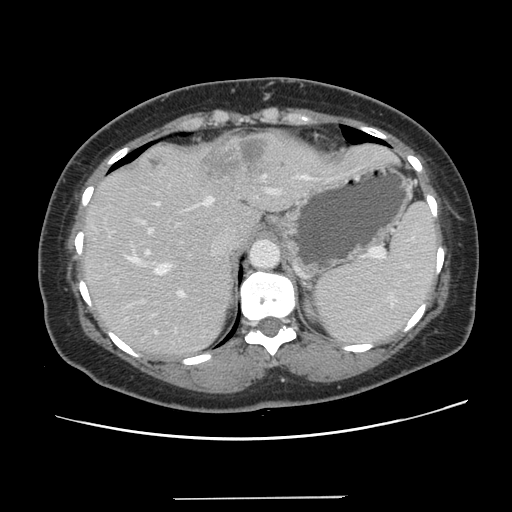
Contrast-enhanced abdominal CT, one axial slice; position 98 of 141 along the scan axis; intravenous contrast given; soft-tissue window (W 400 / L 40 HU); 512 × 512 image matrix, field of view 366 × 366 mm. Female patient, age 53 years. From the clinical record (not read from this slice): diagnosis: colorectal cancer liver metastases, imaged before liver resection; multiple liver metastases: no; largest metastasis: 14.5 cm; disease in both lobes: yes.
Structures marked on this image (expert manual segmentation):
- hepatic veins: bounding box (x1, y1, x2, y2) in pixels: (126, 174, 313, 274)
- liver: (84, 131, 397, 355)
- planned liver remnant (the part of the liver to remain after resection): (84, 209, 261, 356)
- portal vein (with intrahepatic branches): (135, 189, 275, 316)
- liver metastasis: (200, 136, 270, 184)